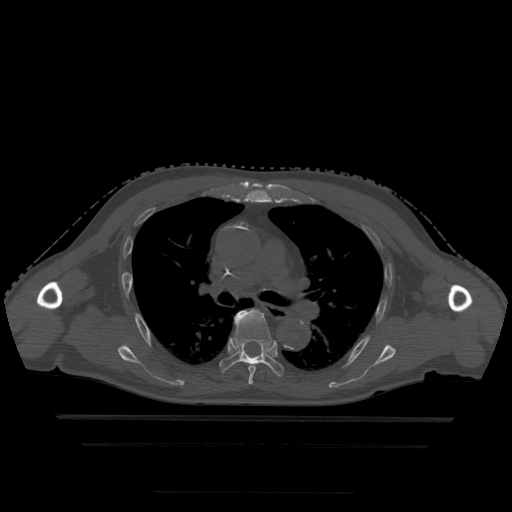
CT including the spine, one axial slice. Position 323 of 522 along the scan axis. Bone window (W 1800 / L 400 HU). 512 × 512 image matrix, field of view 436 × 436 mm. Patient age 68 years. Case-level facts recorded for this patient, not image findings: primary cancer: urothelial.
Structures marked on this image (semi-automatic segmentation, software-assisted and operator-edited):
- T5 vertebra: bounding box [x1, y1, x2, y2] px = [239, 311, 256, 385]
- T6 vertebra: [219, 310, 284, 377]